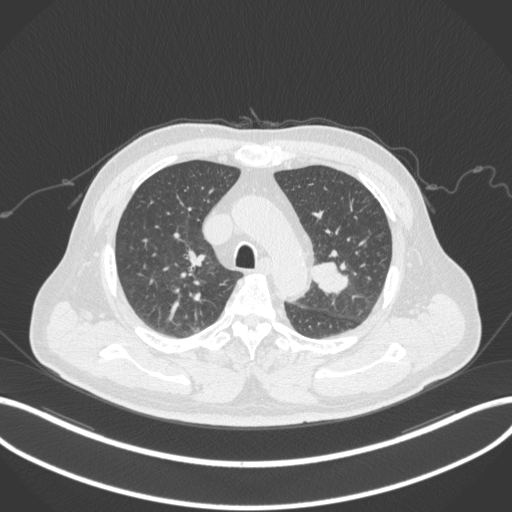
Chest CT, one axial slice; slice 218 of 286 in the series (ordered by position); lung window (W 1500 / L -600 HU); 512 × 512 image matrix, field of view 400 × 400 mm. Male patient, age 67 years. Case-level facts recorded for this patient, not image findings: clinical TNM (as recorded): T2a N1 M0.
Structures marked on this image (bounding box drawn by a radiologist):
- lung tumour (recorded histology: adenocarcinoma): bounding box <307,255,349,296> (left, top, right, bottom; pixels)